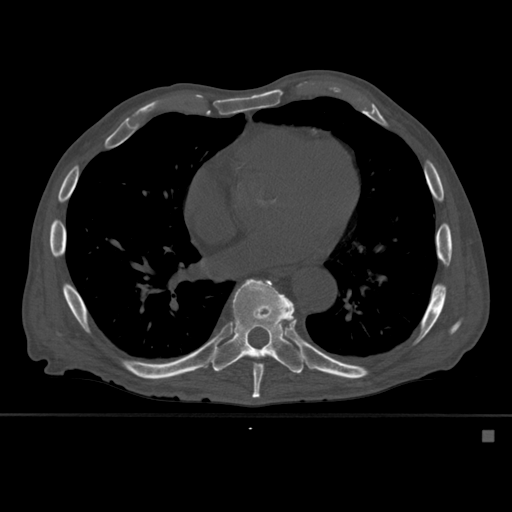
CT including the spine, one axial slice. Position 339 of 527 along the scan axis. Bone window (W 1800 / L 400 HU). 1.5 mm slice thickness. 512 × 512 image matrix, field of view 373 × 373 mm. Male patient, age 78 years. Case-level facts recorded for this patient, not image findings: primary cancer: prostate.
Outlined on this slice (semi-automatically segmented with operator editing):
- T8 vertebra: box from (x=249, y=279) to (x=264, y=398) px
- T9 vertebra: (x=213, y=279)–(x=306, y=376)